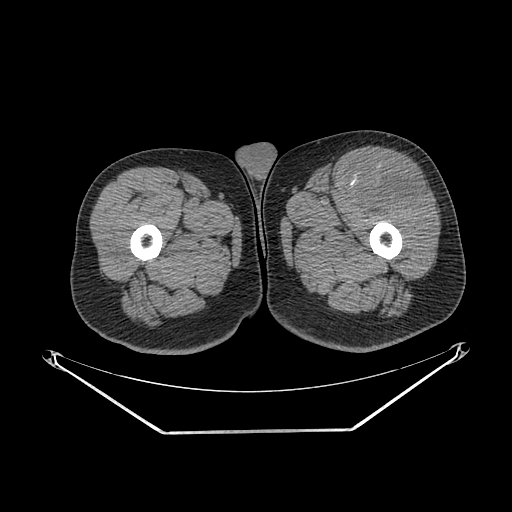
CT of an extremity soft-tissue mass (from a PET/CT study), one axial slice. Slice 247 of 267 in the series (ordered by position). Reconstruction kernel SOFT. Soft-tissue window (W 400 / L 40 HU). 3.75 mm slice thickness. 512 × 512 image matrix, field of view 500 × 500 mm. Male patient. Case-level facts recorded for this patient, not image findings: histological type: extraskeletal osteosarcoma; grade: high; site of the primary tumour: thigh.
Structures marked on this image (expert contour drawn on MRI and transferred to this co-registered scan by the dataset authors):
- gross tumour volume (mass): box from (x=356, y=164) to (x=426, y=209) px